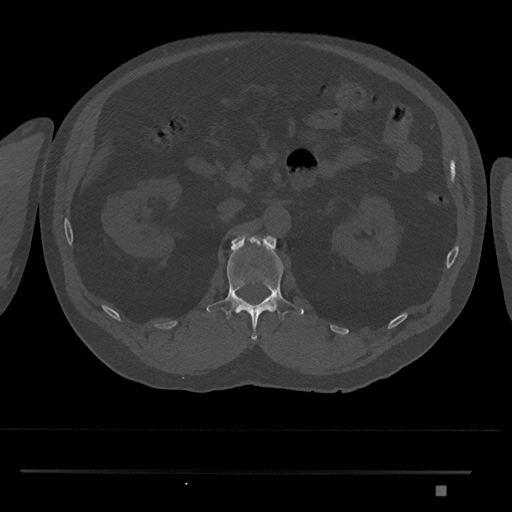
CT including the spine, one axial slice. Position 819 of 1134 along the scan axis. Bone window (W 1800 / L 400 HU). 0.5 mm slice thickness. 512 × 512 image matrix, field of view 429 × 429 mm. Patient: male, 65 years. From the clinical record (not read from this slice): primary cancer: prostate.
Outlined on this slice (semi-automatically segmented with operator editing):
- L1 vertebra: bounding box (x1, y1, x2, y2) in pixels: (206, 234, 304, 341)